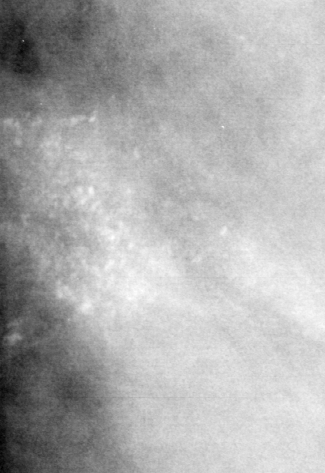
Cropped region of a digitized screen-film mammogram centred on a radiologist-marked abnormality; left breast; CC view.
Marked abnormality: calcifications, morphology pleomorphic, distribution clustered; BI-RADS assessment category 4; subtlety rating 3 on a 1 (subtle) to 5 (obvious) scale; pathology (as recorded): malignant.